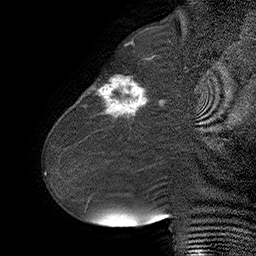
Breast MRI (dynamic contrast-enhanced), one sagittal slice. Position 20 of 55 along the scan axis. Dynamic contrast-enhanced series, time point 2 of 6 at this slice position (early post-contrast). 1.5 T. TE 4.5 ms, TR 32.4 ms. 256 × 256 image matrix, field of view 180 × 180 mm. Female patient. Case-level facts recorded for this patient, not image findings: setting: breast cancer imaged before/during neoadjuvant chemotherapy; receptor status: HER2-positive.
Structures marked on this image (semi-automatic segmentation, software-assisted and operator-edited):
- analysis volume of interest (the breast-tissue region the enhancement analysis was run in; not a lesion): bounding box [x1, y1, x2, y2] px = [80, 64, 163, 134]
- tumour enhancement mask (voxels above the 100 % enhancement threshold inside the analysis volume of interest): [93, 77, 162, 118]